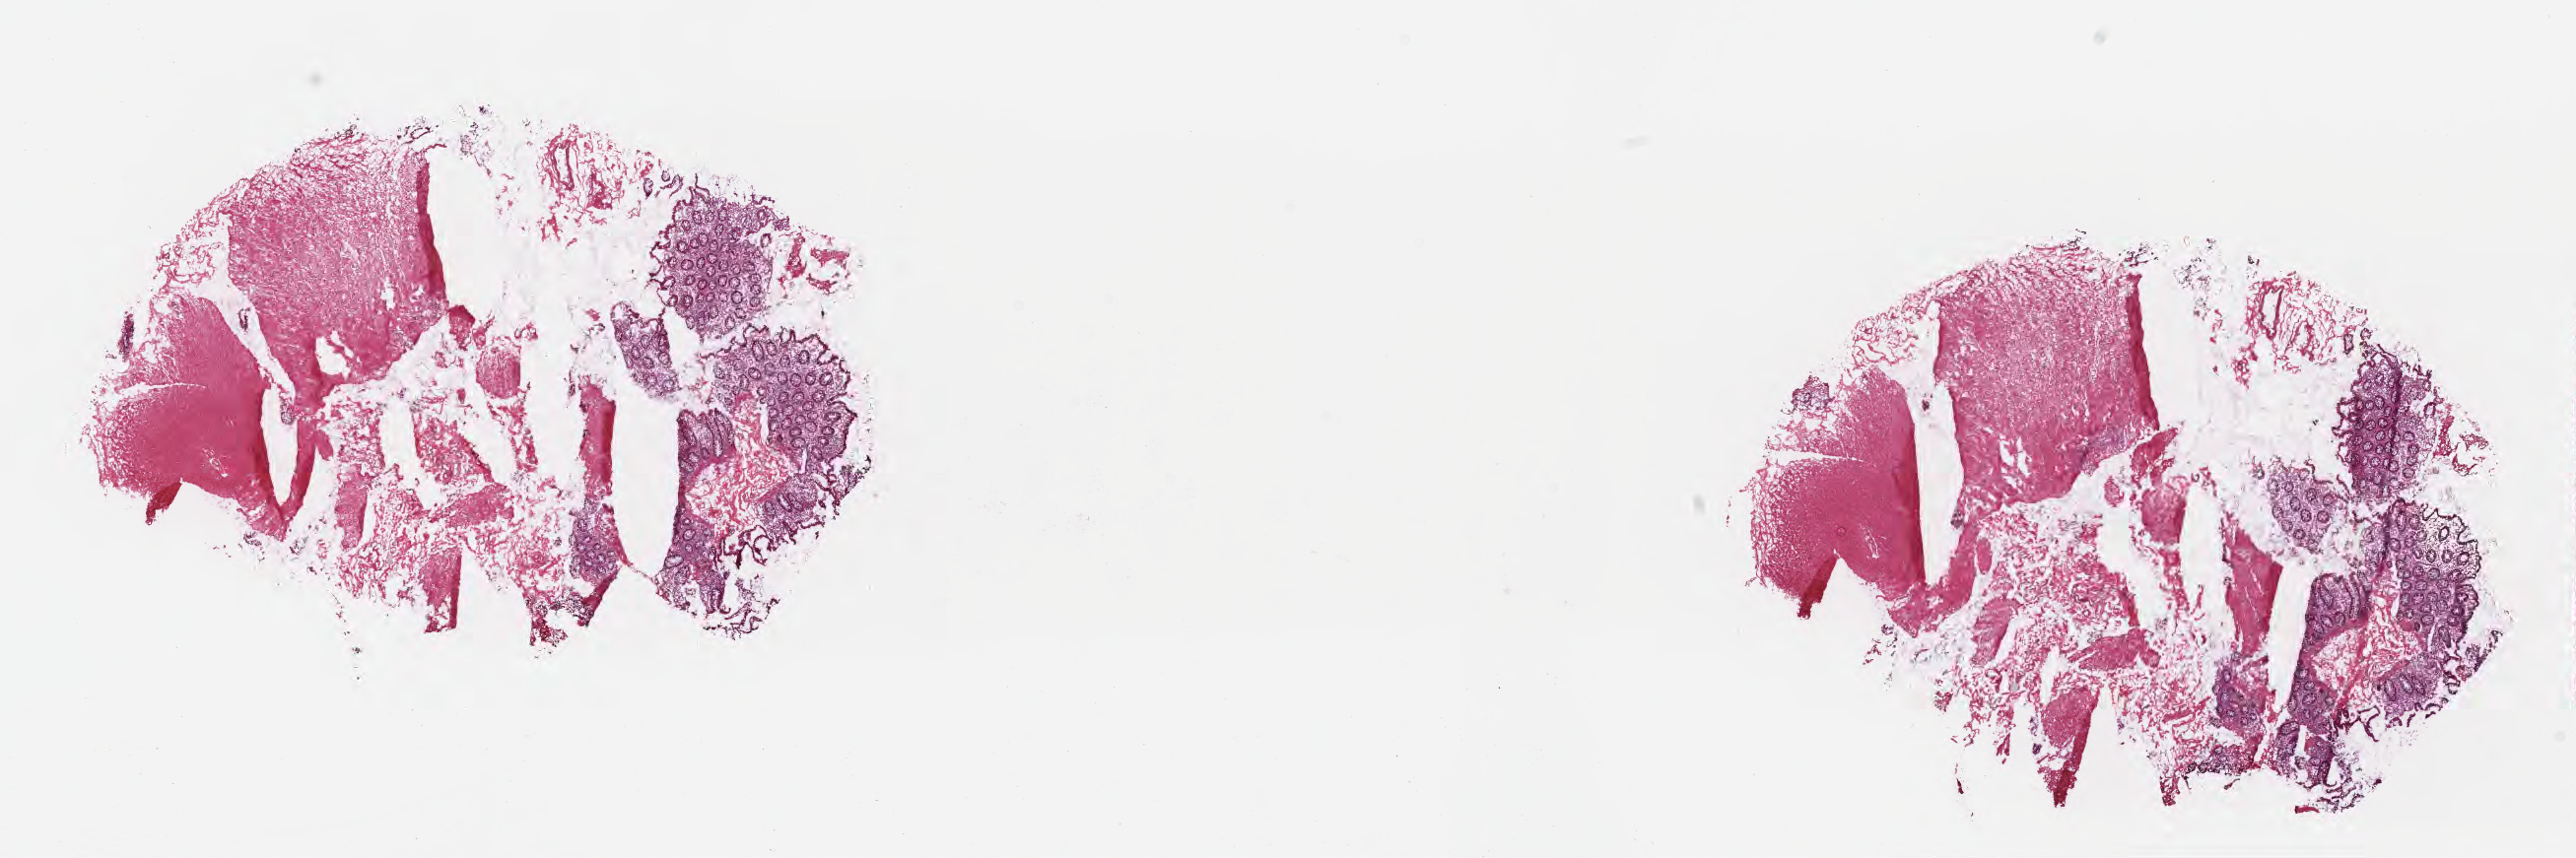
Whole-slide image, H&E stain, a low-resolution overview of the entire scanned area, about 21.1 x 7.0 mm; cryosection; normal-tissue sample (non-tumor) from a patient with medullary carcinoma, NOS; site: splenic flexure of colon. Female, age 81 years at initial diagnosis.
This section: non-tumor tissue sample; the patient's diagnosis is given above.